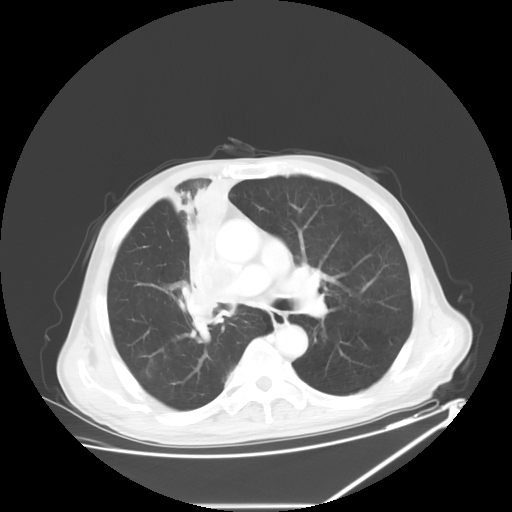
Chest CT, one axial slice; slice 37 of 60 in the series (ordered by position); reconstruction kernel STANDARD; 120 kVp; lung window (W 1500 / L -600 HU); 5 mm slice thickness; 512 × 512 image matrix. Male patient, age 73 years. Case-level facts recorded for this patient, not image findings: clinical TNM (as recorded): T2a N1 M0.
Structures marked on this image (rectangle marked by the reading radiologist):
- lung tumour (recorded histology: squamous cell carcinoma): box from (x=181, y=174) to (x=245, y=344) px